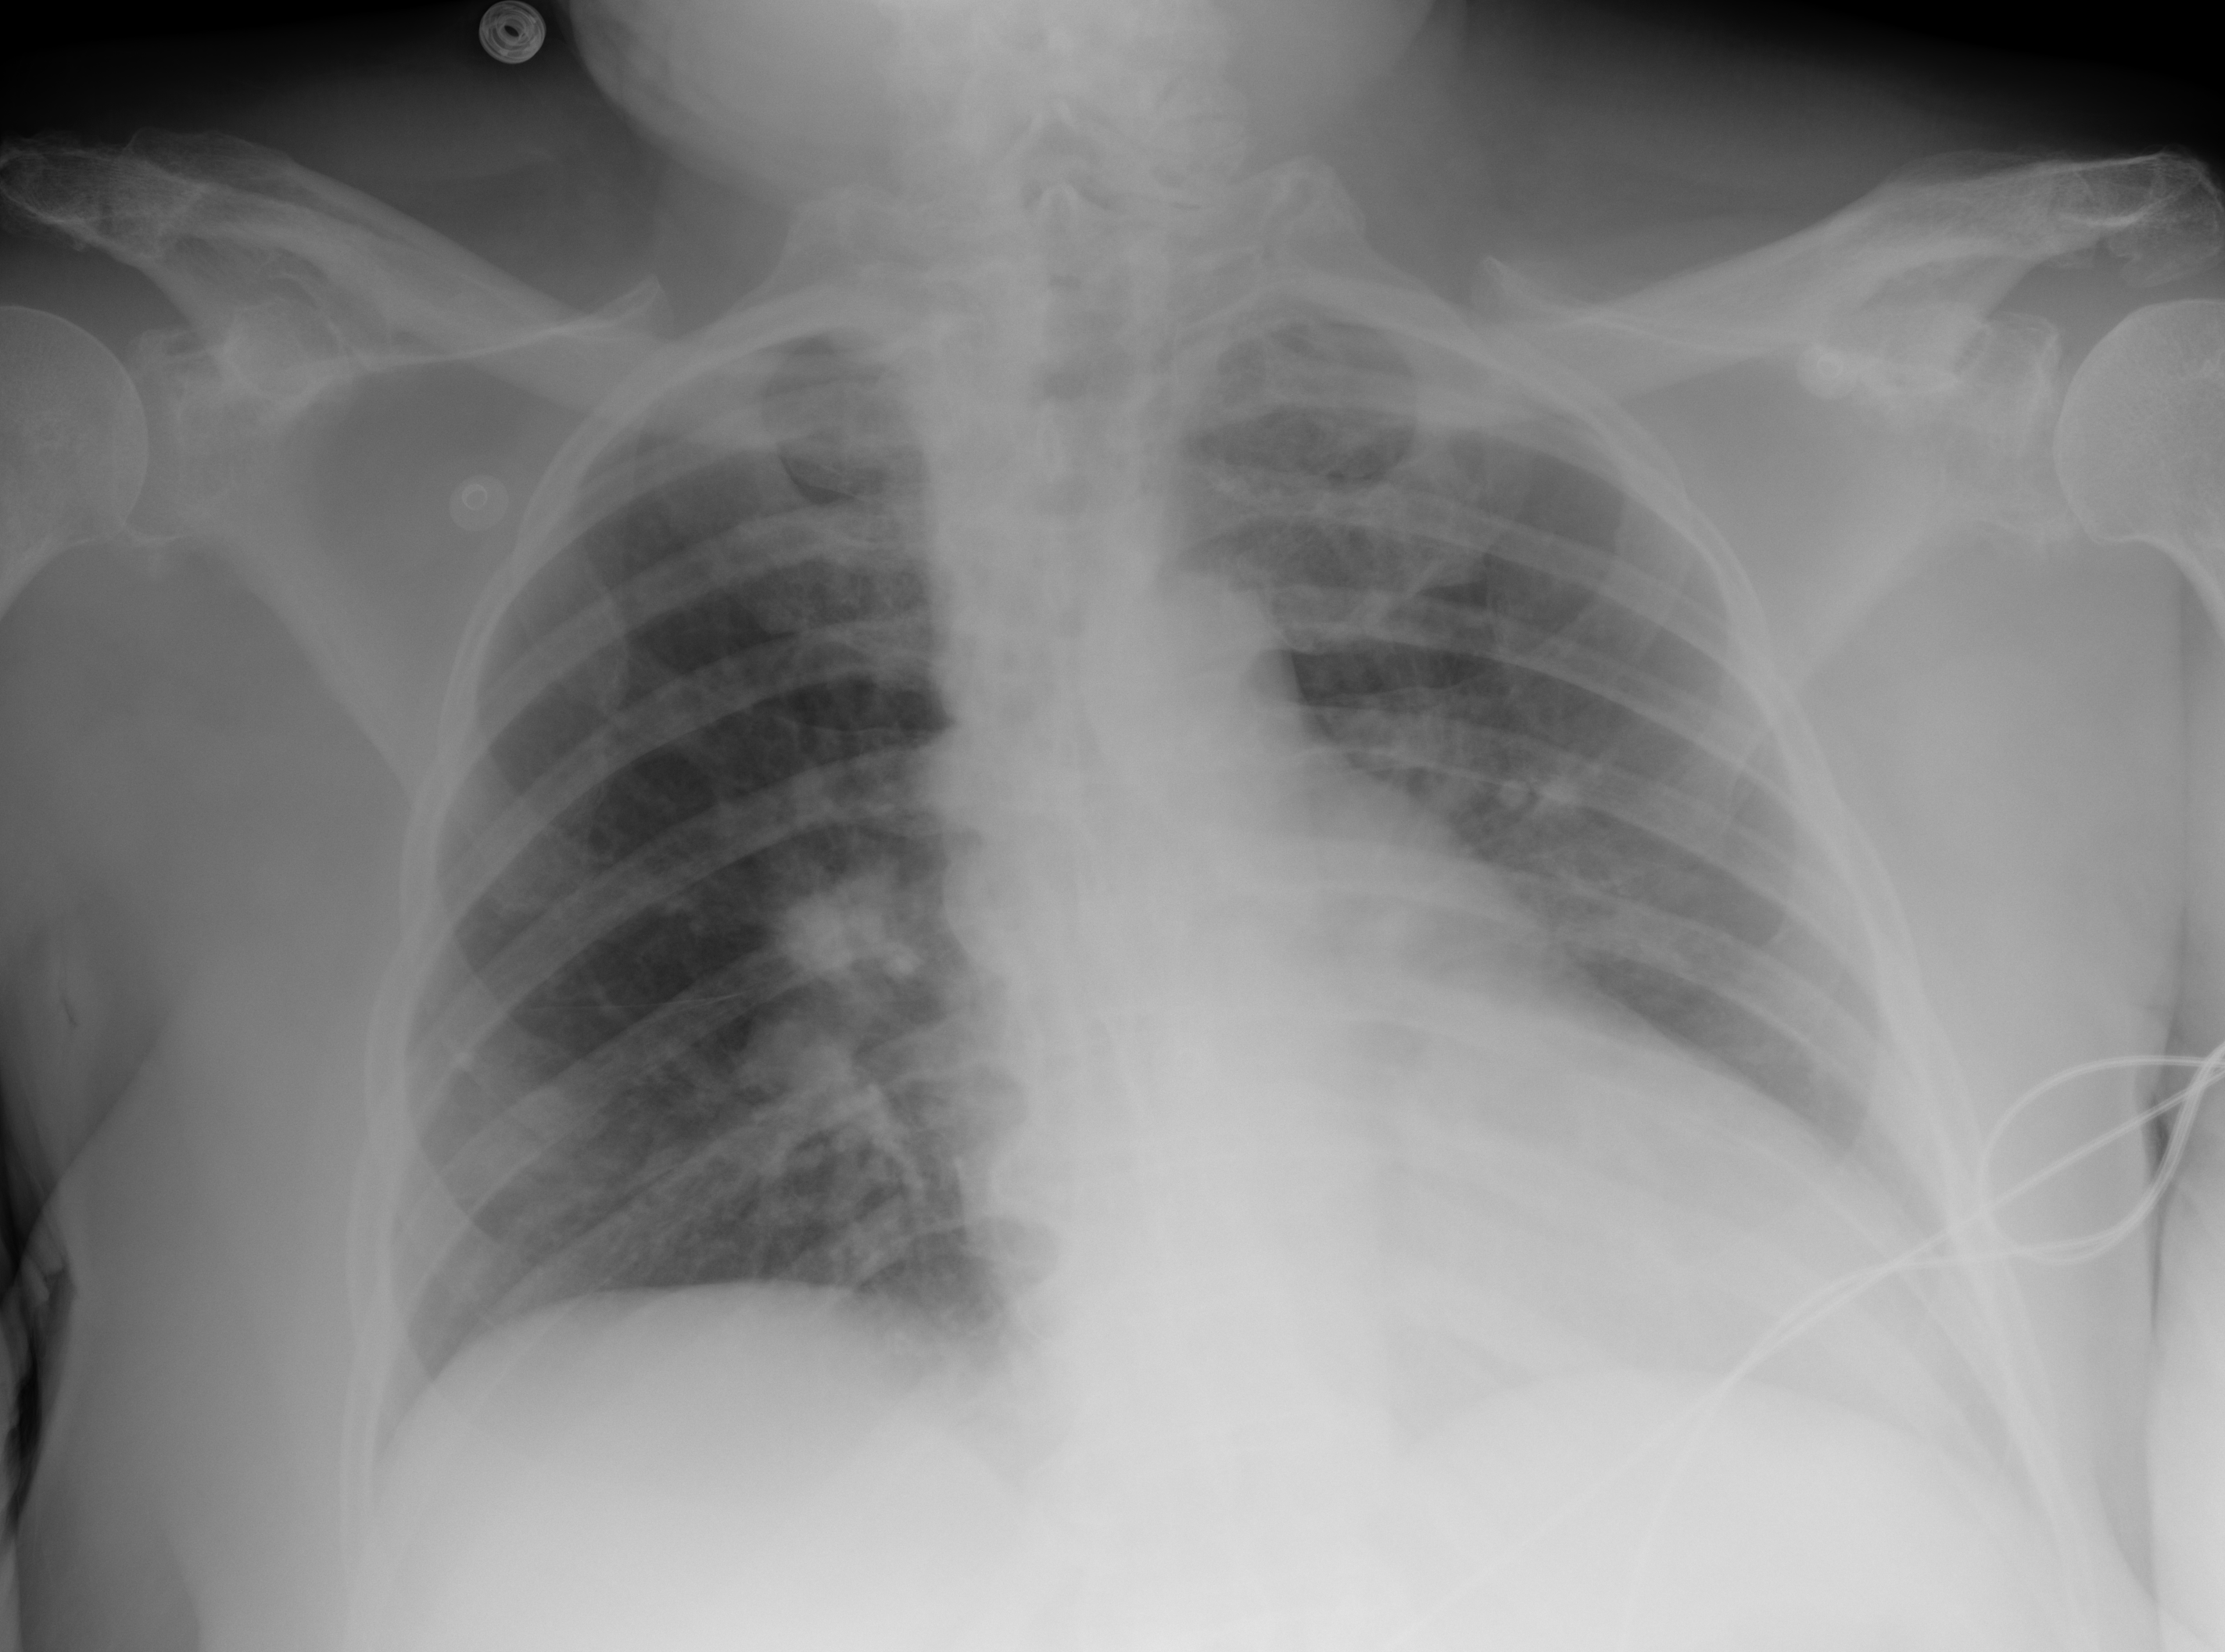
Chest X-ray (portable), AP projection. Female patient, age 69 years; imaged 0 days after the COVID-19 diagnosis.
Radiologist key findings (as recorded): The lungs appear clear with no evidence of airspace consolidation.